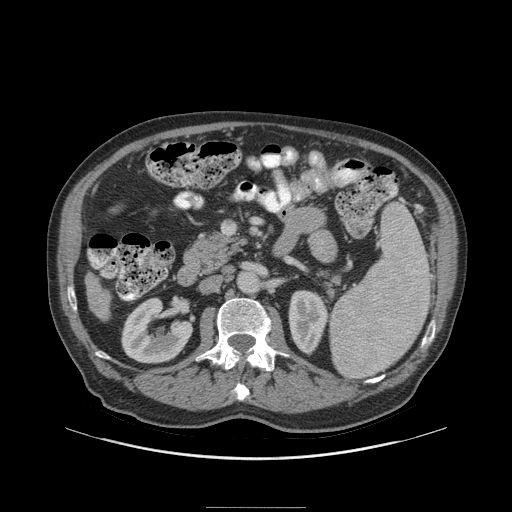
Contrast-enhanced abdominal CT (liver protocol), one axial slice; position 28 of 105 along the scan axis; reconstruction kernel STANDARD; 140 kVp; soft-tissue window (W 400 / L 40 HU); 512 × 512 image matrix, field of view 440 × 440 mm. Case-level facts recorded for this patient, not image findings: diagnosis: hepatocellular carcinoma (patient treated with transarterial chemoembolisation; whether this scan precedes or follows treatment is not stated here); TNM stage (as recorded): Stage-I; Child-Pugh class: A; tumour size: 5.1 cm.
Outlined on this slice (semi-automatically segmented with operator editing):
- liver parenchyma outside the tumour (the mass and vessels are separate outlines, so this box may not span the whole liver): bounding box <84,273,110,320> (left, top, right, bottom; pixels)